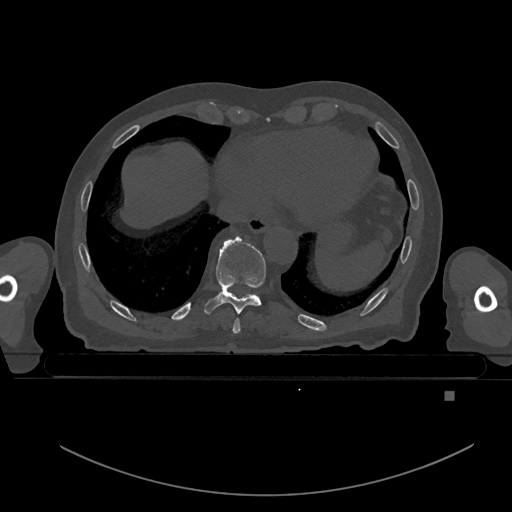
CT including the spine, one axial slice. Slice 144 of 969 in the series (ordered by position). Bone window (W 1800 / L 400 HU). 0.5 mm slice thickness. 512 × 512 image matrix, field of view 456 × 456 mm. Male patient, age 82 years. From the clinical record (not read from this slice): primary cancer: prostate; vertebrae with lytic lesions (as recorded): T11, T9, T8, T2.
Outlined on this slice (semi-automatically segmented with operator editing):
- T8 vertebra: bounding box (x1, y1, x2, y2) in pixels: (233, 318, 241, 334)
- T9 vertebra: (204, 237, 266, 314)